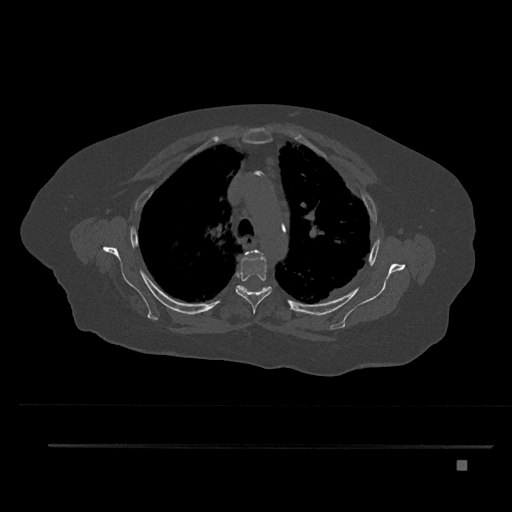
CT including the spine, one axial slice; position 600 of 797 along the scan axis; reconstruction kernel Br40s/3; 120 kVp; bone window (W 1800 / L 400 HU); 512 × 512 image matrix, field of view 437 × 437 mm. Patient: female, 76 years. From the clinical record (not read from this slice): primary cancer: lung; vertebrae with lytic lesions (as recorded): T11, L3.
Annotated regions visible in this slice (semi-automatic segmentation, software-assisted and operator-edited):
- T3 vertebra: bounding box [x1, y1, x2, y2] px = [244, 250, 260, 258]
- T4 vertebra: [235, 250, 272, 314]
- T5 vertebra: [237, 284, 269, 293]